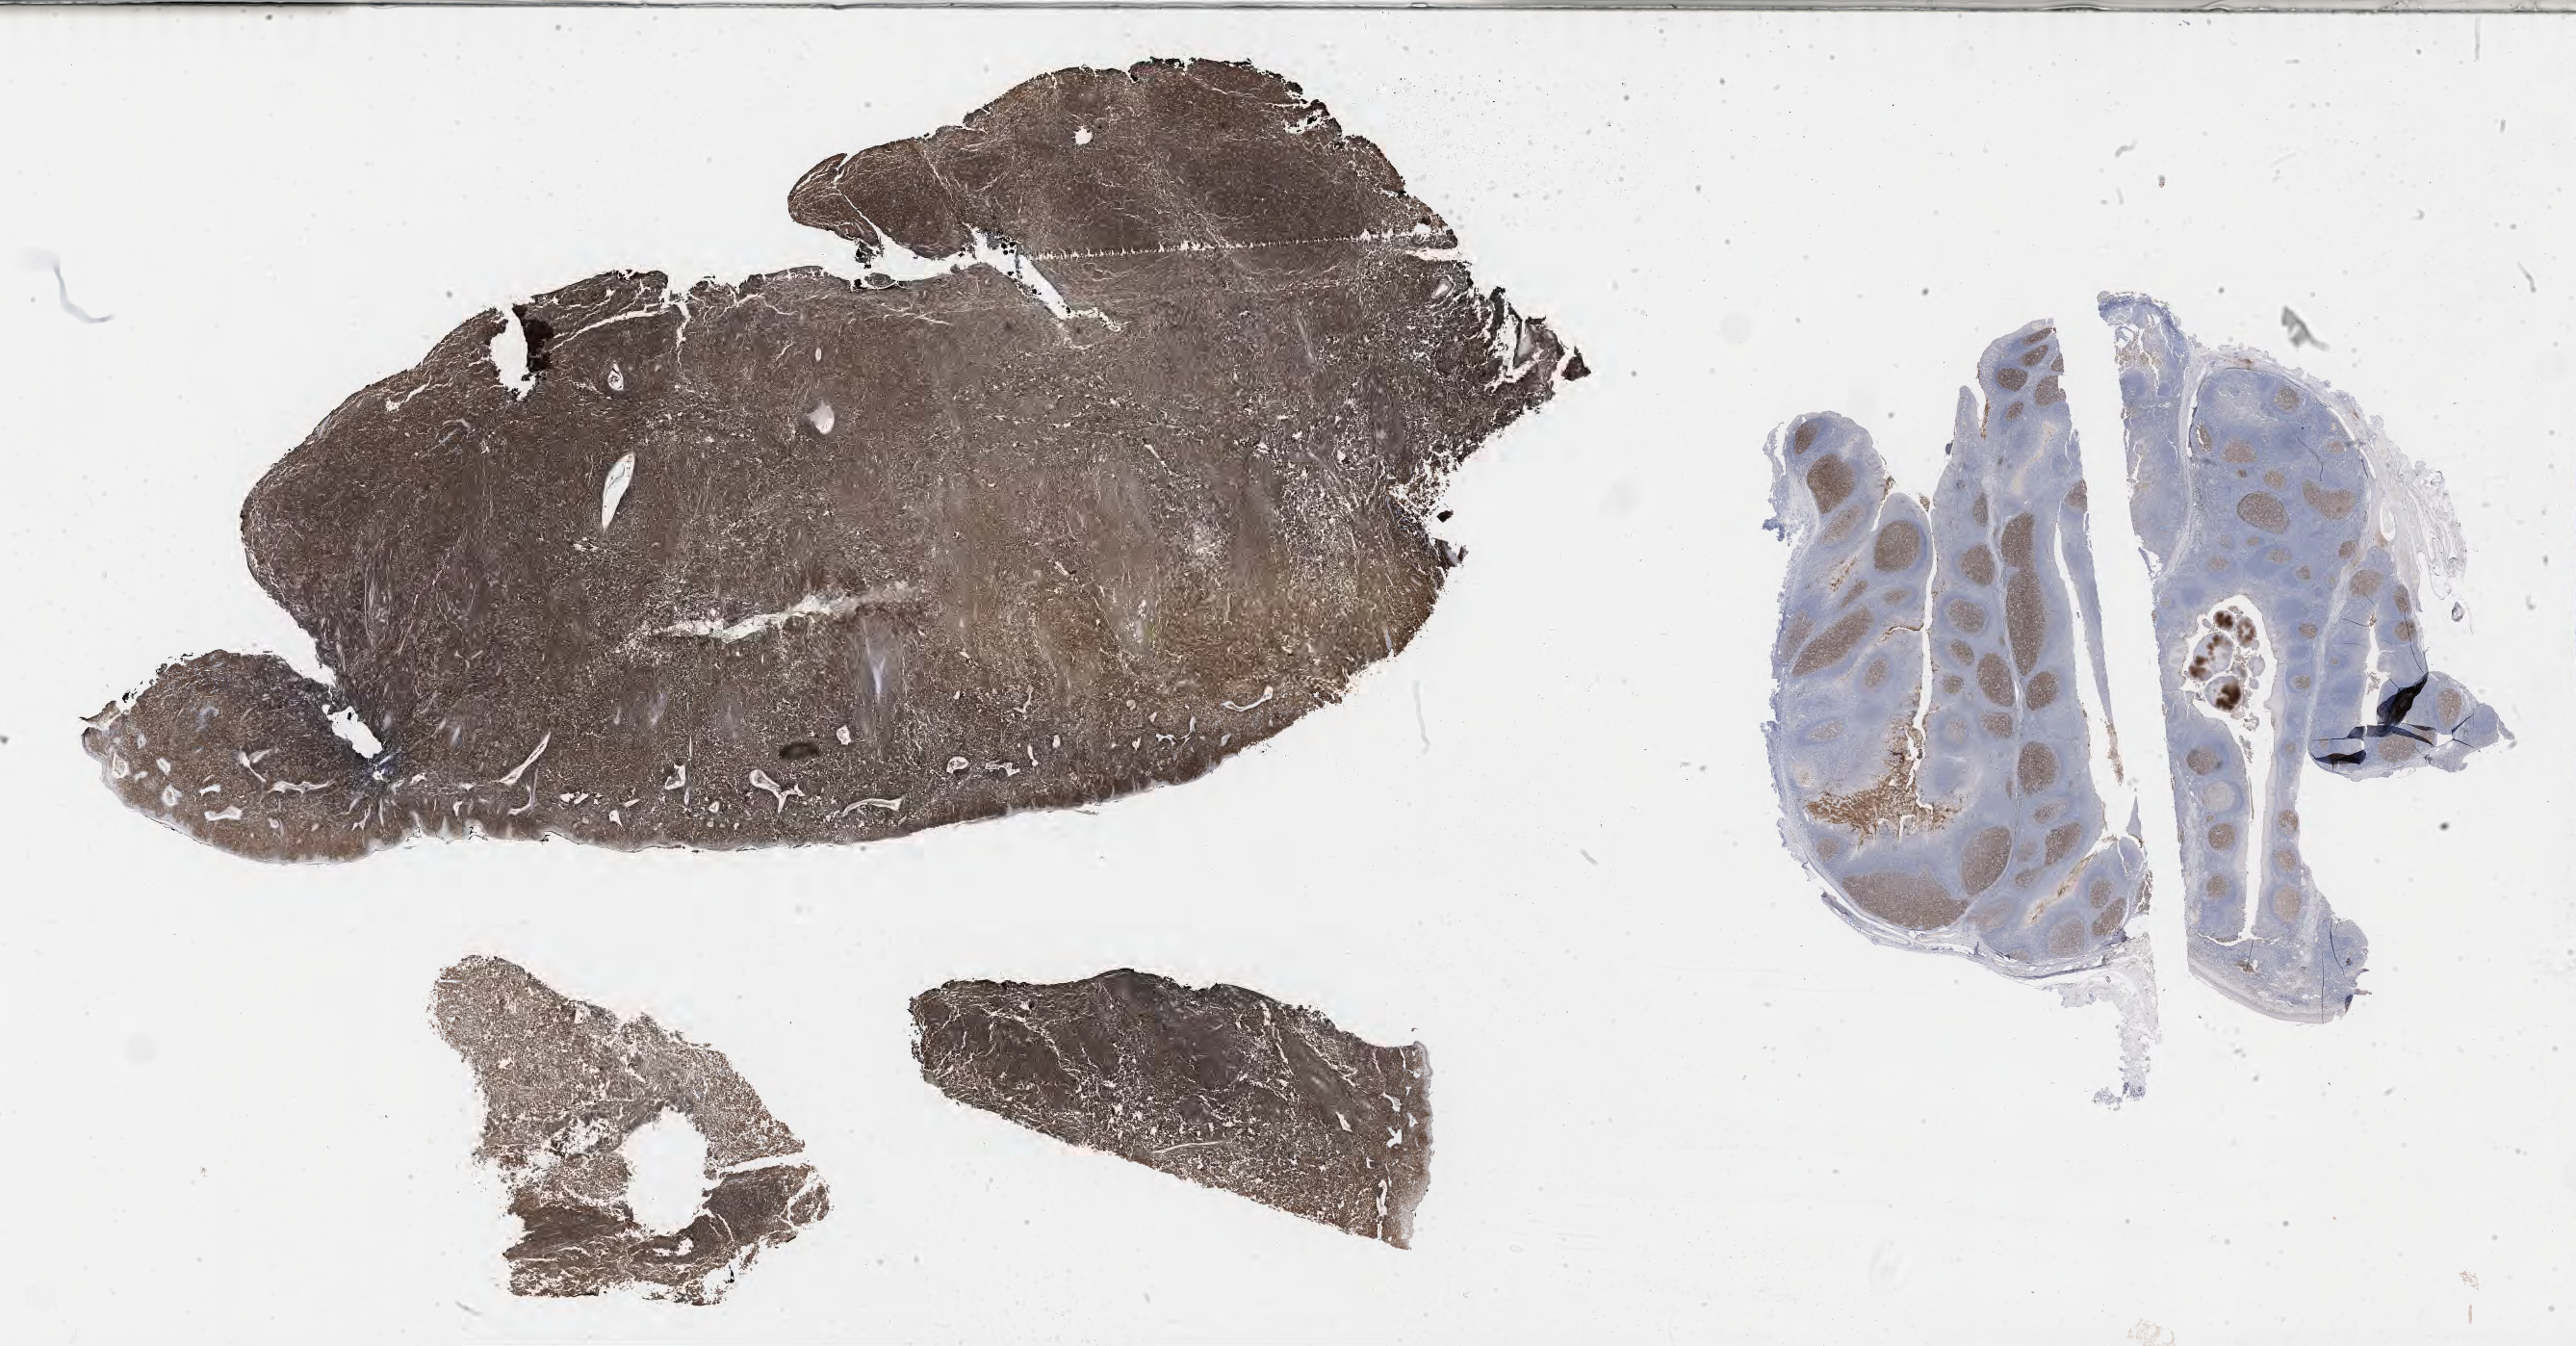
Immunohistochemistry (IHC) whole-slide image stained for CD10 — whole scanned area (about 43.3 x 22.6 mm) shown as a low-resolution overview, tumor tissue. Male patient, aged 46.
Histologic diagnosis: Burkitt lymphoma, NOS.